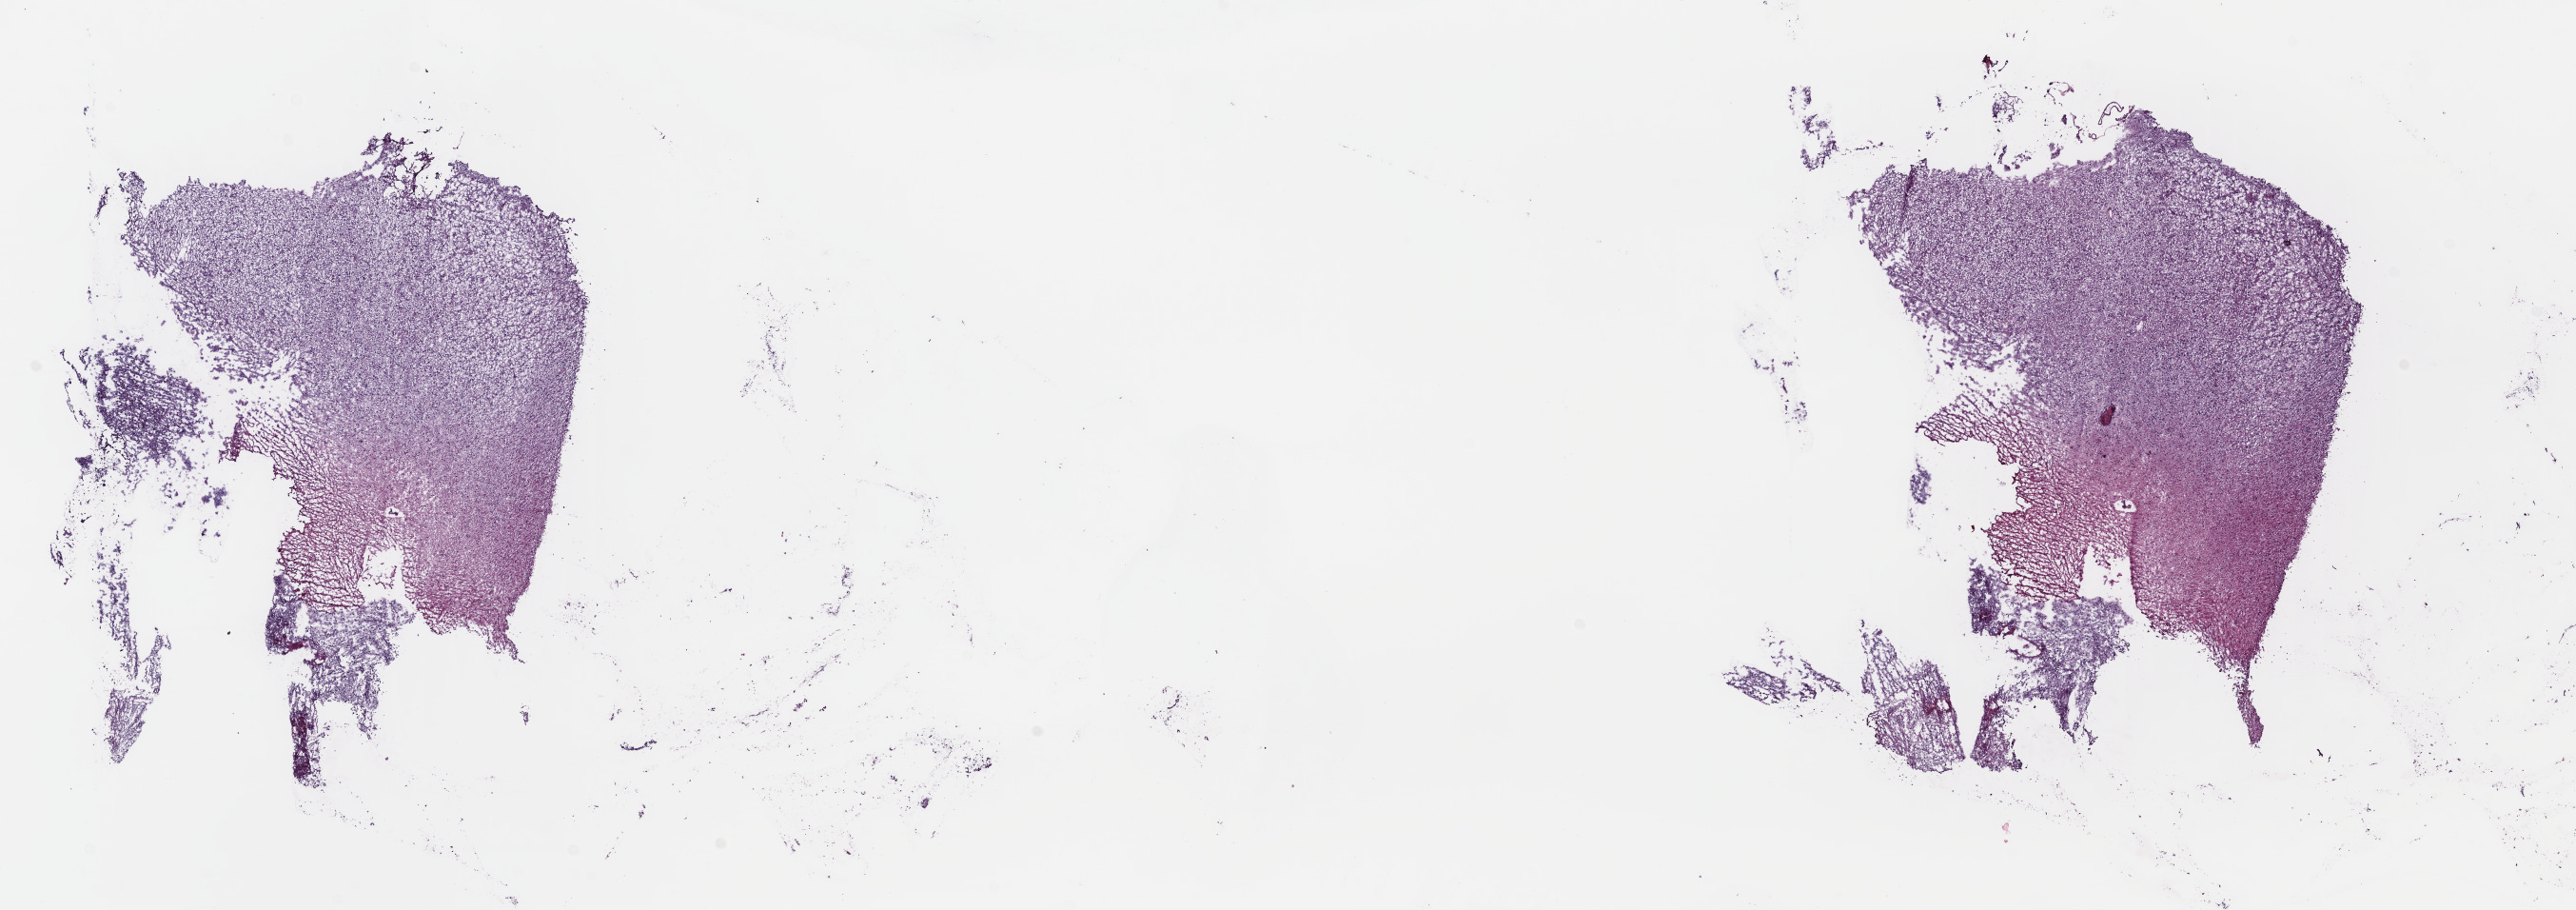
H&E-stained whole-slide image, whole scanned area (about 21.3 x 7.5 mm, slide scanned at 40x) shown as a low-resolution overview; frozen section from the top of the tissue portion; sample: primary tumour, brain. Male patient; age at initial diagnosis 30 years. Composition of this section per pathologist review: tumour cells 80%, tumour nuclei 80%.
Pathologic diagnosis: Mixed glioma (temporal lobe).